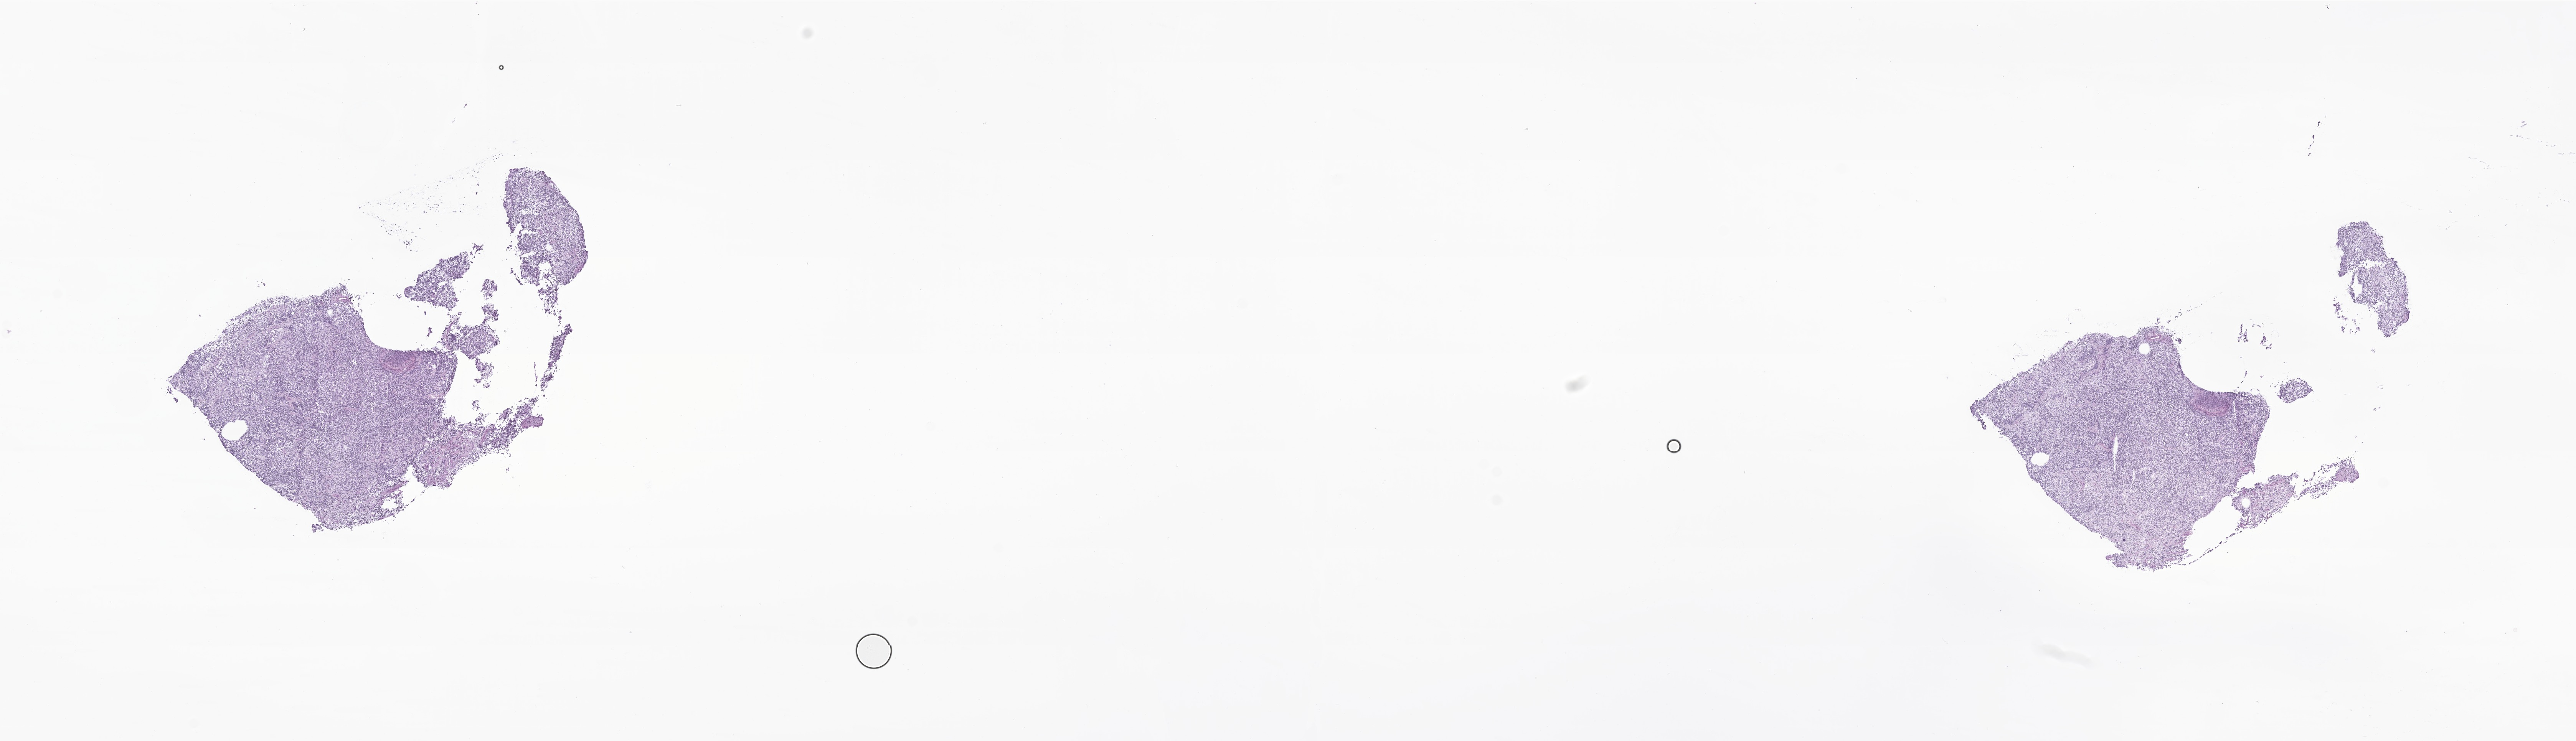
H&E whole-slide image of tumor tissue from the brain — a low-resolution overview of the entire scanned area, about 28.3 x 8.1 mm. Cryosection (OCT / tissue freezing medium). Patient male; age 68 months (5 years 8 months).
* diagnosis: Medulloblastoma, NOS